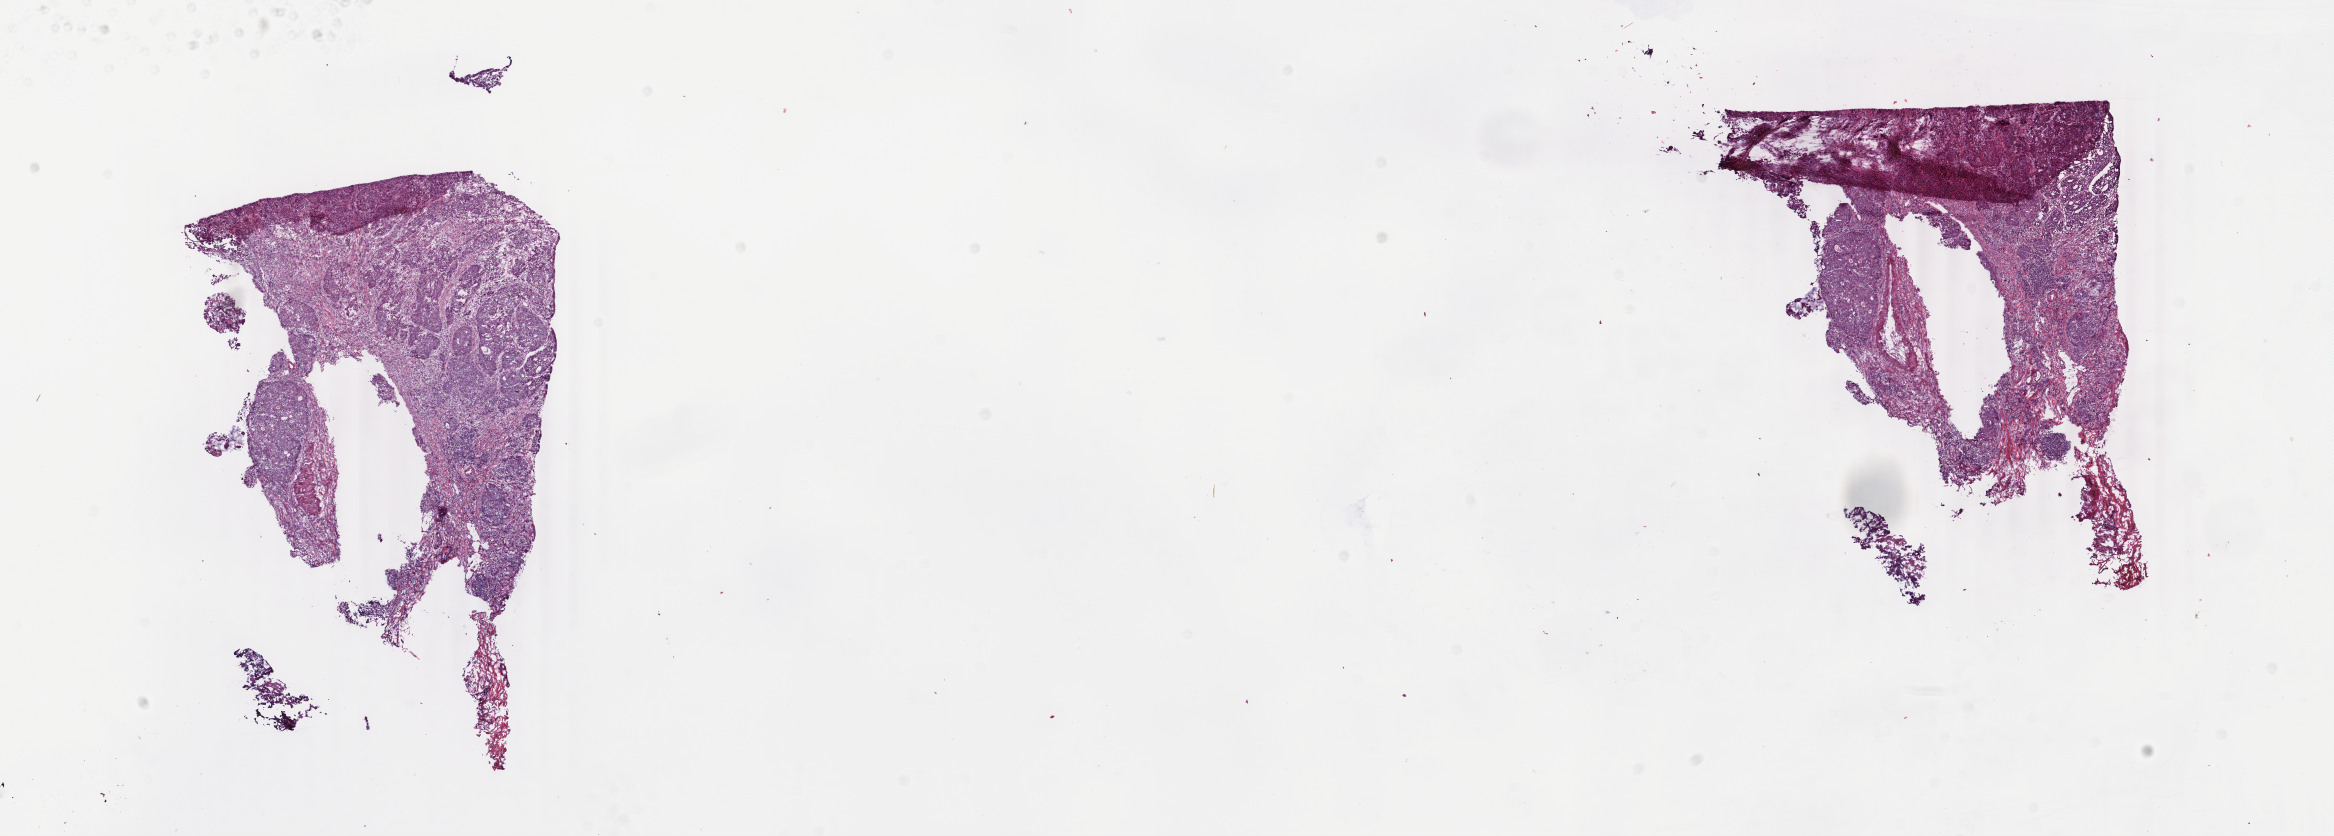
Digitized Hematoxylin and eosin (H&E) stained tissue section (whole slide), low-resolution overview of the scanned area, about 18.6 x 6.6 mm (from a 40x scan), frozen section, sample: primary tumour, rectum. Male, age 80 years at initial diagnosis. Slide review estimates, as recorded: tumour cells 85%, tumour nuclei 85%, normal cells 0%, stromal cells 14%, necrosis 1%. Infiltration values recorded for this section: lymphocyte infiltration 7%, monocyte infiltration 3%, neutrophil infiltration 1%.
AJCC pathologic stage: IIA. Lymph nodes positive (case pathology): 0 of 14 examined. Histologic diagnosis: Adenocarcinoma, NOS.